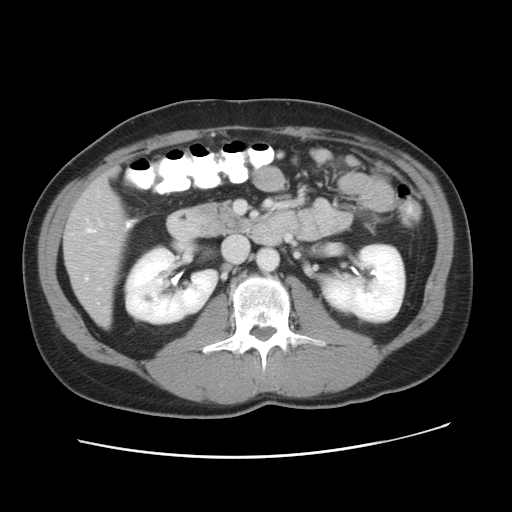
Contrast-enhanced abdominal CT, one axial slice; 120 kVp; soft-tissue window (W 400 / L 40 HU); 512 × 512 image matrix, field of view 363 × 363 mm. Male patient, age 41 years. From the clinical record (not read from this slice): diagnosis: colorectal cancer liver metastases, imaged before liver resection; multiple liver metastases: yes; largest metastasis: 0.7 cm; disease in both lobes: yes.
Structures marked on this image (expert manual segmentation):
- hepatic veins: bounding box <85,227,95,280> (left, top, right, bottom; pixels)
- liver: <66,174,126,326>
- portal vein (with intrahepatic branches): <100,241,103,243>